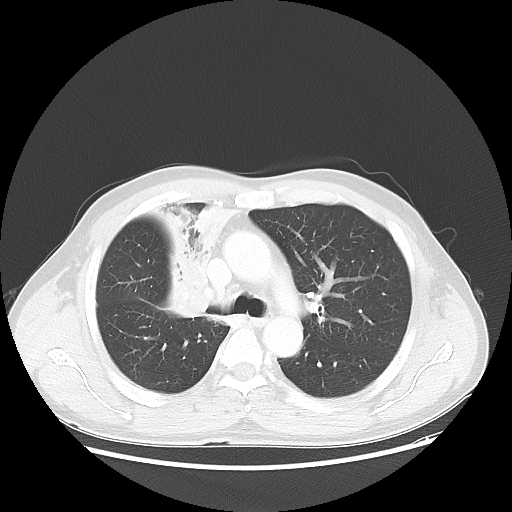
Chest CT, one axial slice. Reconstruction kernel LUNG. Lung window (W 1500 / L -600 HU). 5 mm slice thickness. 512 × 512 image matrix. Patient: male, 60 years. From the clinical record (not read from this slice): clinical TNM (as recorded): T2a N1 M0.
Structures marked on this image (bounding box drawn by a radiologist):
- lung tumour (recorded histology: squamous cell carcinoma): bounding box <139,193,240,324> (left, top, right, bottom; pixels)